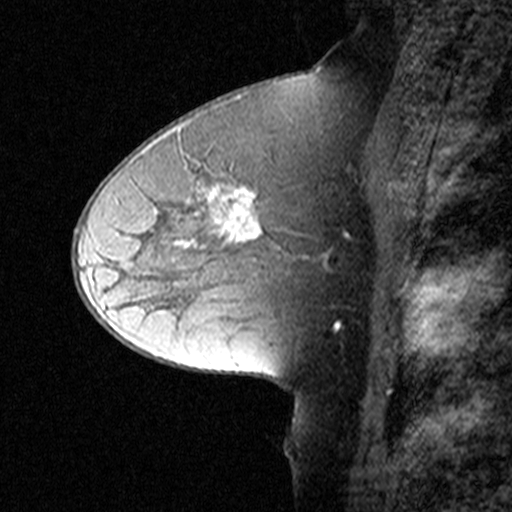
Breast MRI (dynamic contrast-enhanced), one sagittal slice; slice 24 of 44 in the series (ordered by position); dynamic contrast-enhanced study with each time point stored as its own series, time point 2 of 3 at this slice position (early post-contrast, ordered by acquisition time); 1.5 T; TE 4.5 ms, TR 11 ms; 3 mm slice thickness; 512 × 512 image matrix, field of view 200 × 200 mm. Female patient, age 50 years. Case-level facts recorded for this patient, not image findings: setting: breast cancer imaged before/during neoadjuvant chemotherapy; receptor status: HR-positive, HER2-negative.
Structures marked on this image (semi-automatically segmented with operator editing):
- analysis volume of interest (the breast-tissue region the enhancement analysis was run in; not a lesion): bounding box <126,162,329,291> (left, top, right, bottom; pixels)
- tumour enhancement mask (voxels above the 90 % enhancement threshold inside the analysis volume of interest): <174,186,262,242>